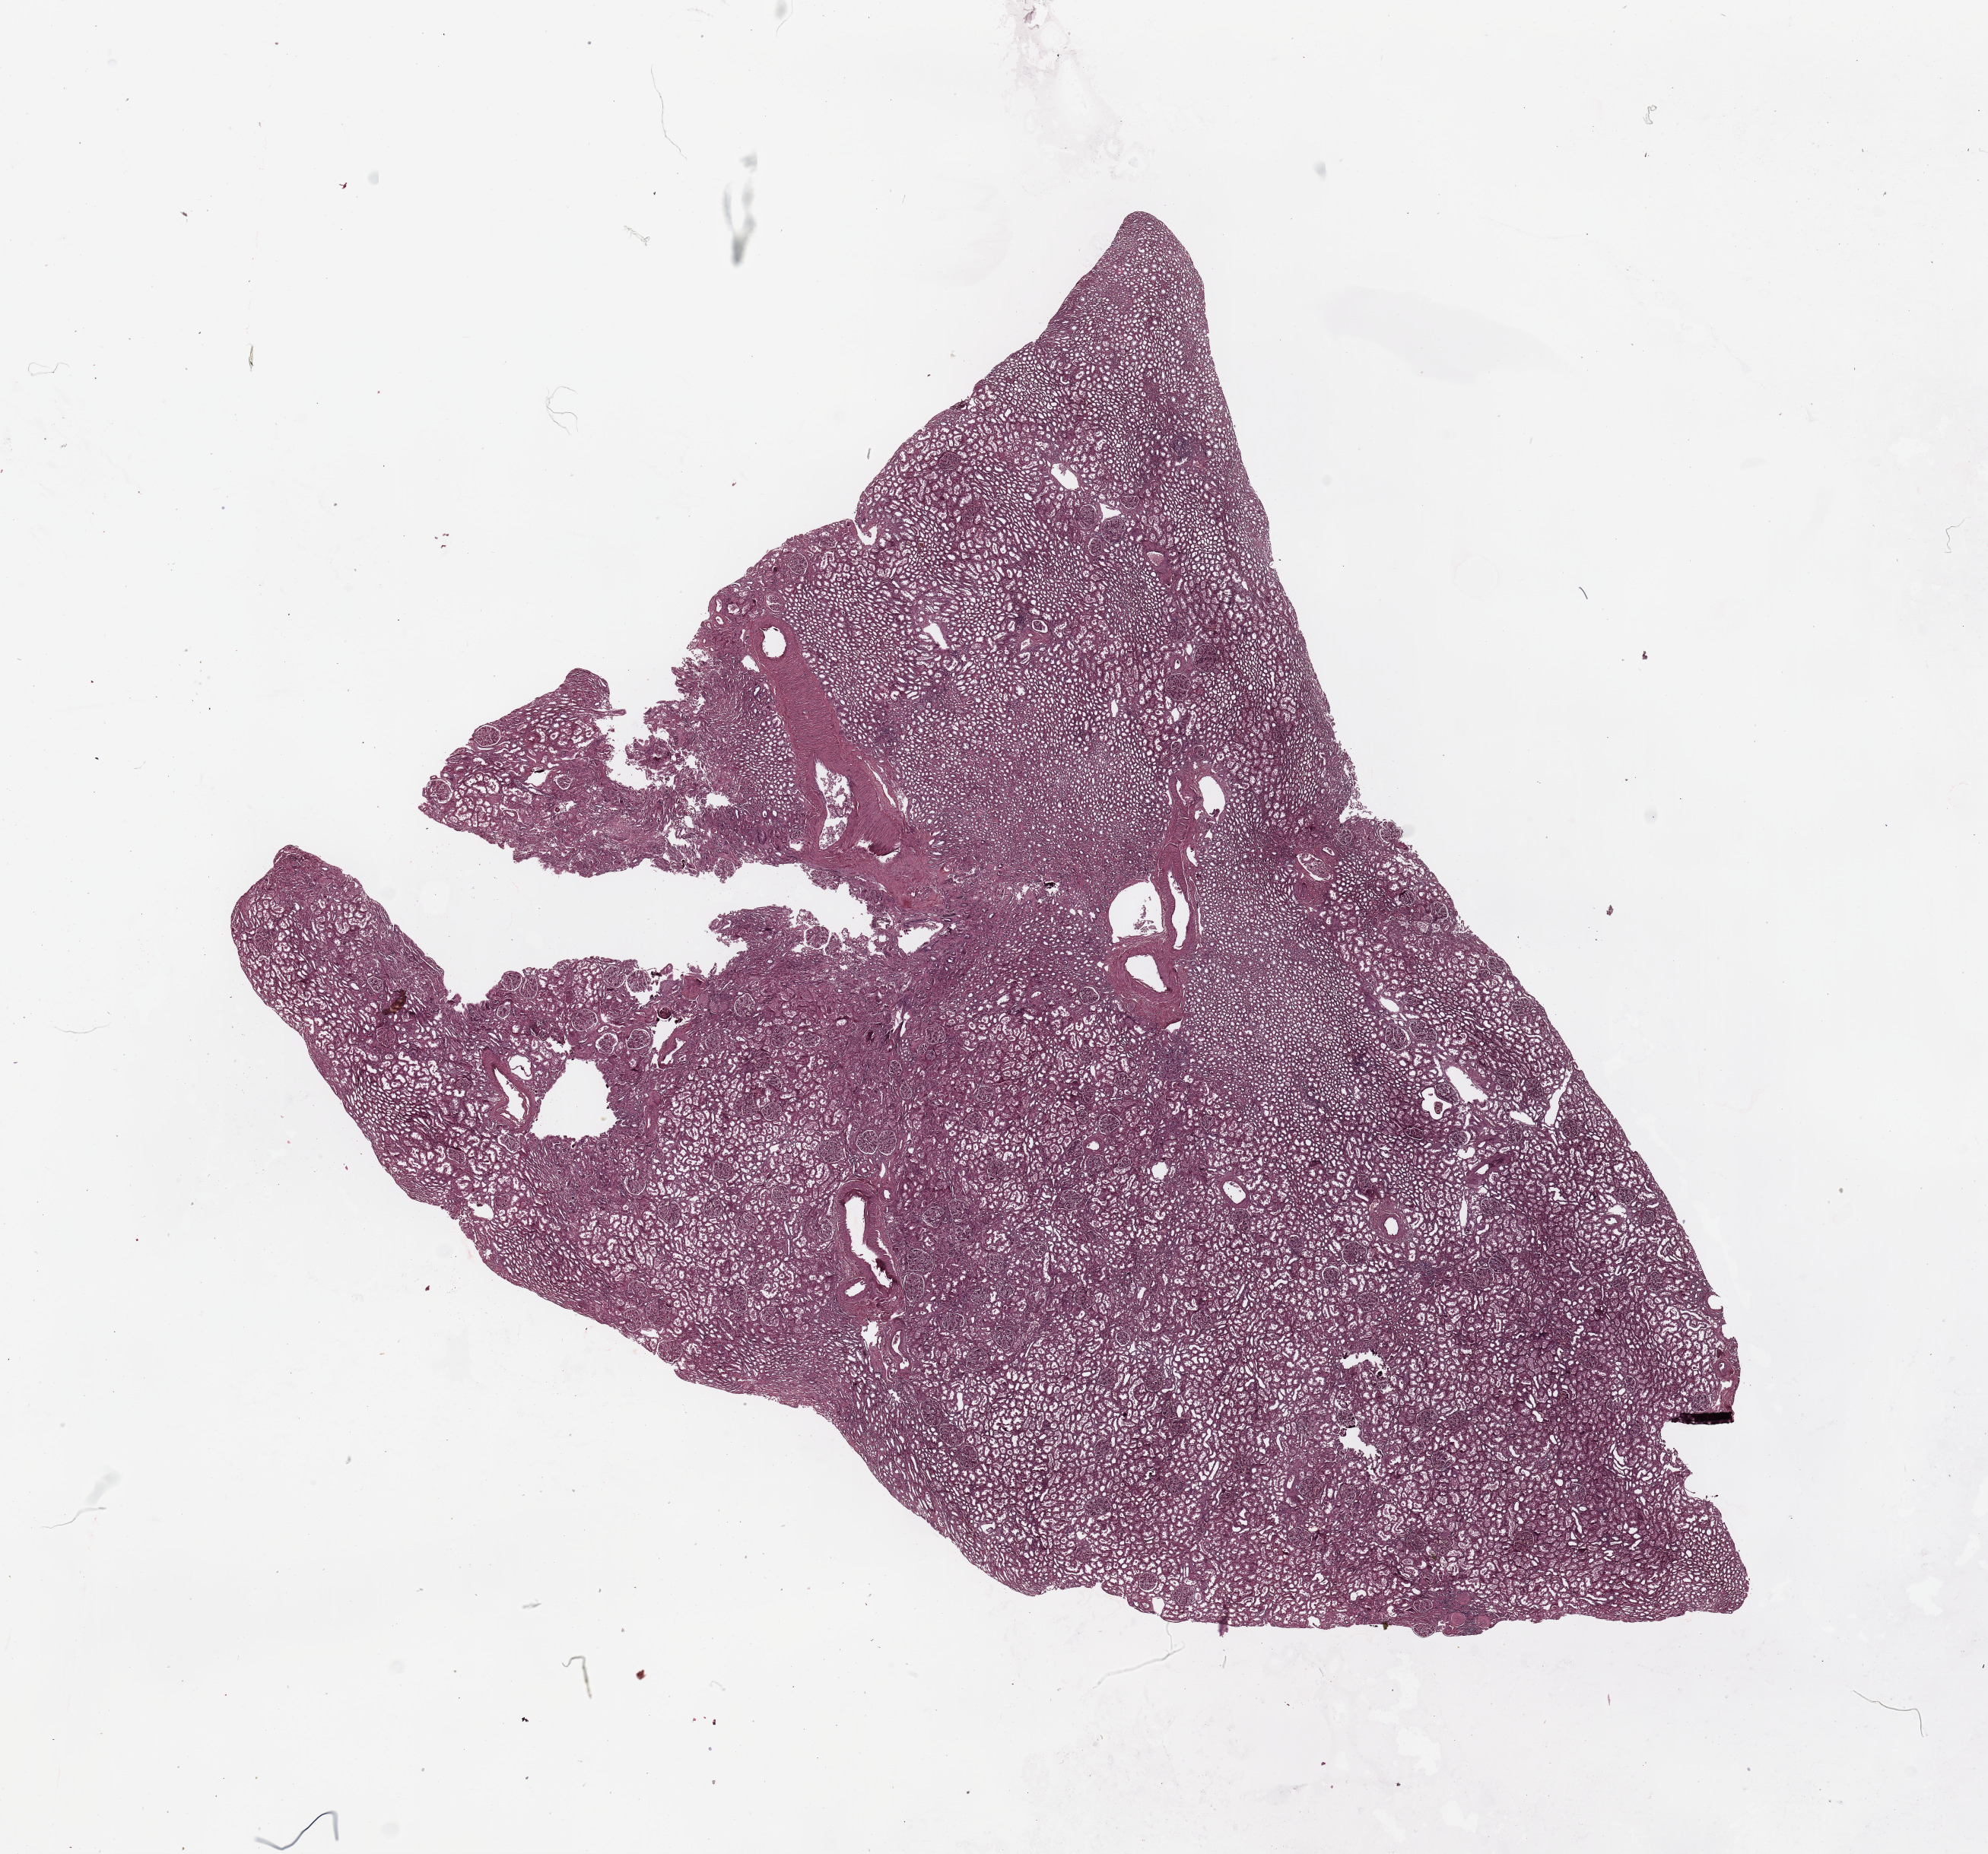
Whole-slide histology image, H&E-stained — low-resolution overview of the scanned area, about 20.7 x 19.3 mm (from a 20x scan). Normal (non-tumour) tissue sample, sampled site: kidney. Patient: male, age 51 years.
This section: normal (non-tumour) tissue from the same patient. Patient diagnosis: Renal cell carcinoma, NOS.